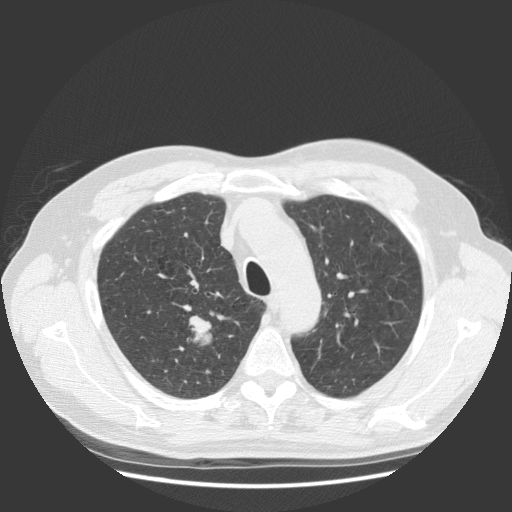
Low-dose screening chest CT, one axial slice; position 97 of 131 along the scan axis; 140 kVp; lung window (W 1500 / L -600 HU); 2.5 mm slice thickness; 512 × 512 image matrix, field of view 369 × 369 mm.
Structures marked on this image (expert manual segmentation):
- lesion 1 (tumor, upper lobe of right lung): bounding box <187,316,212,345> (left, top, right, bottom; pixels)